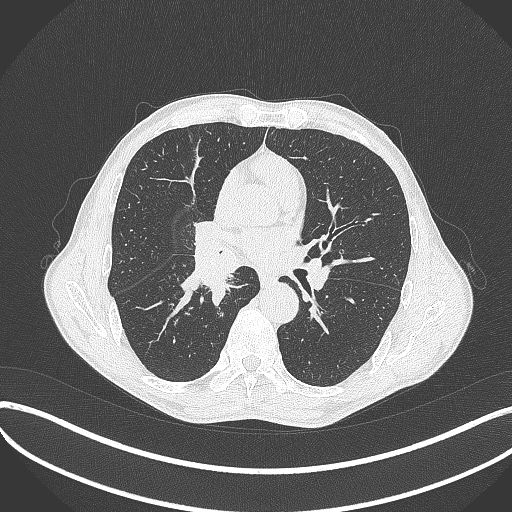
Chest CT, one axial slice; slice 230 of 481 in the series (ordered by position); reconstruction kernel B70f; 120 kVp; lung window (W 1500 / L -600 HU); 512 × 512 image matrix, field of view 400 × 400 mm. Patient: male, 65 years. From the clinical record (not read from this slice): clinical TNM (as recorded): T2a N0 M0.
Structures marked on this image (bounding box drawn by a radiologist):
- lung tumour (recorded histology: squamous cell carcinoma): bounding box (x1, y1, x2, y2) in pixels: (184, 220, 238, 306)